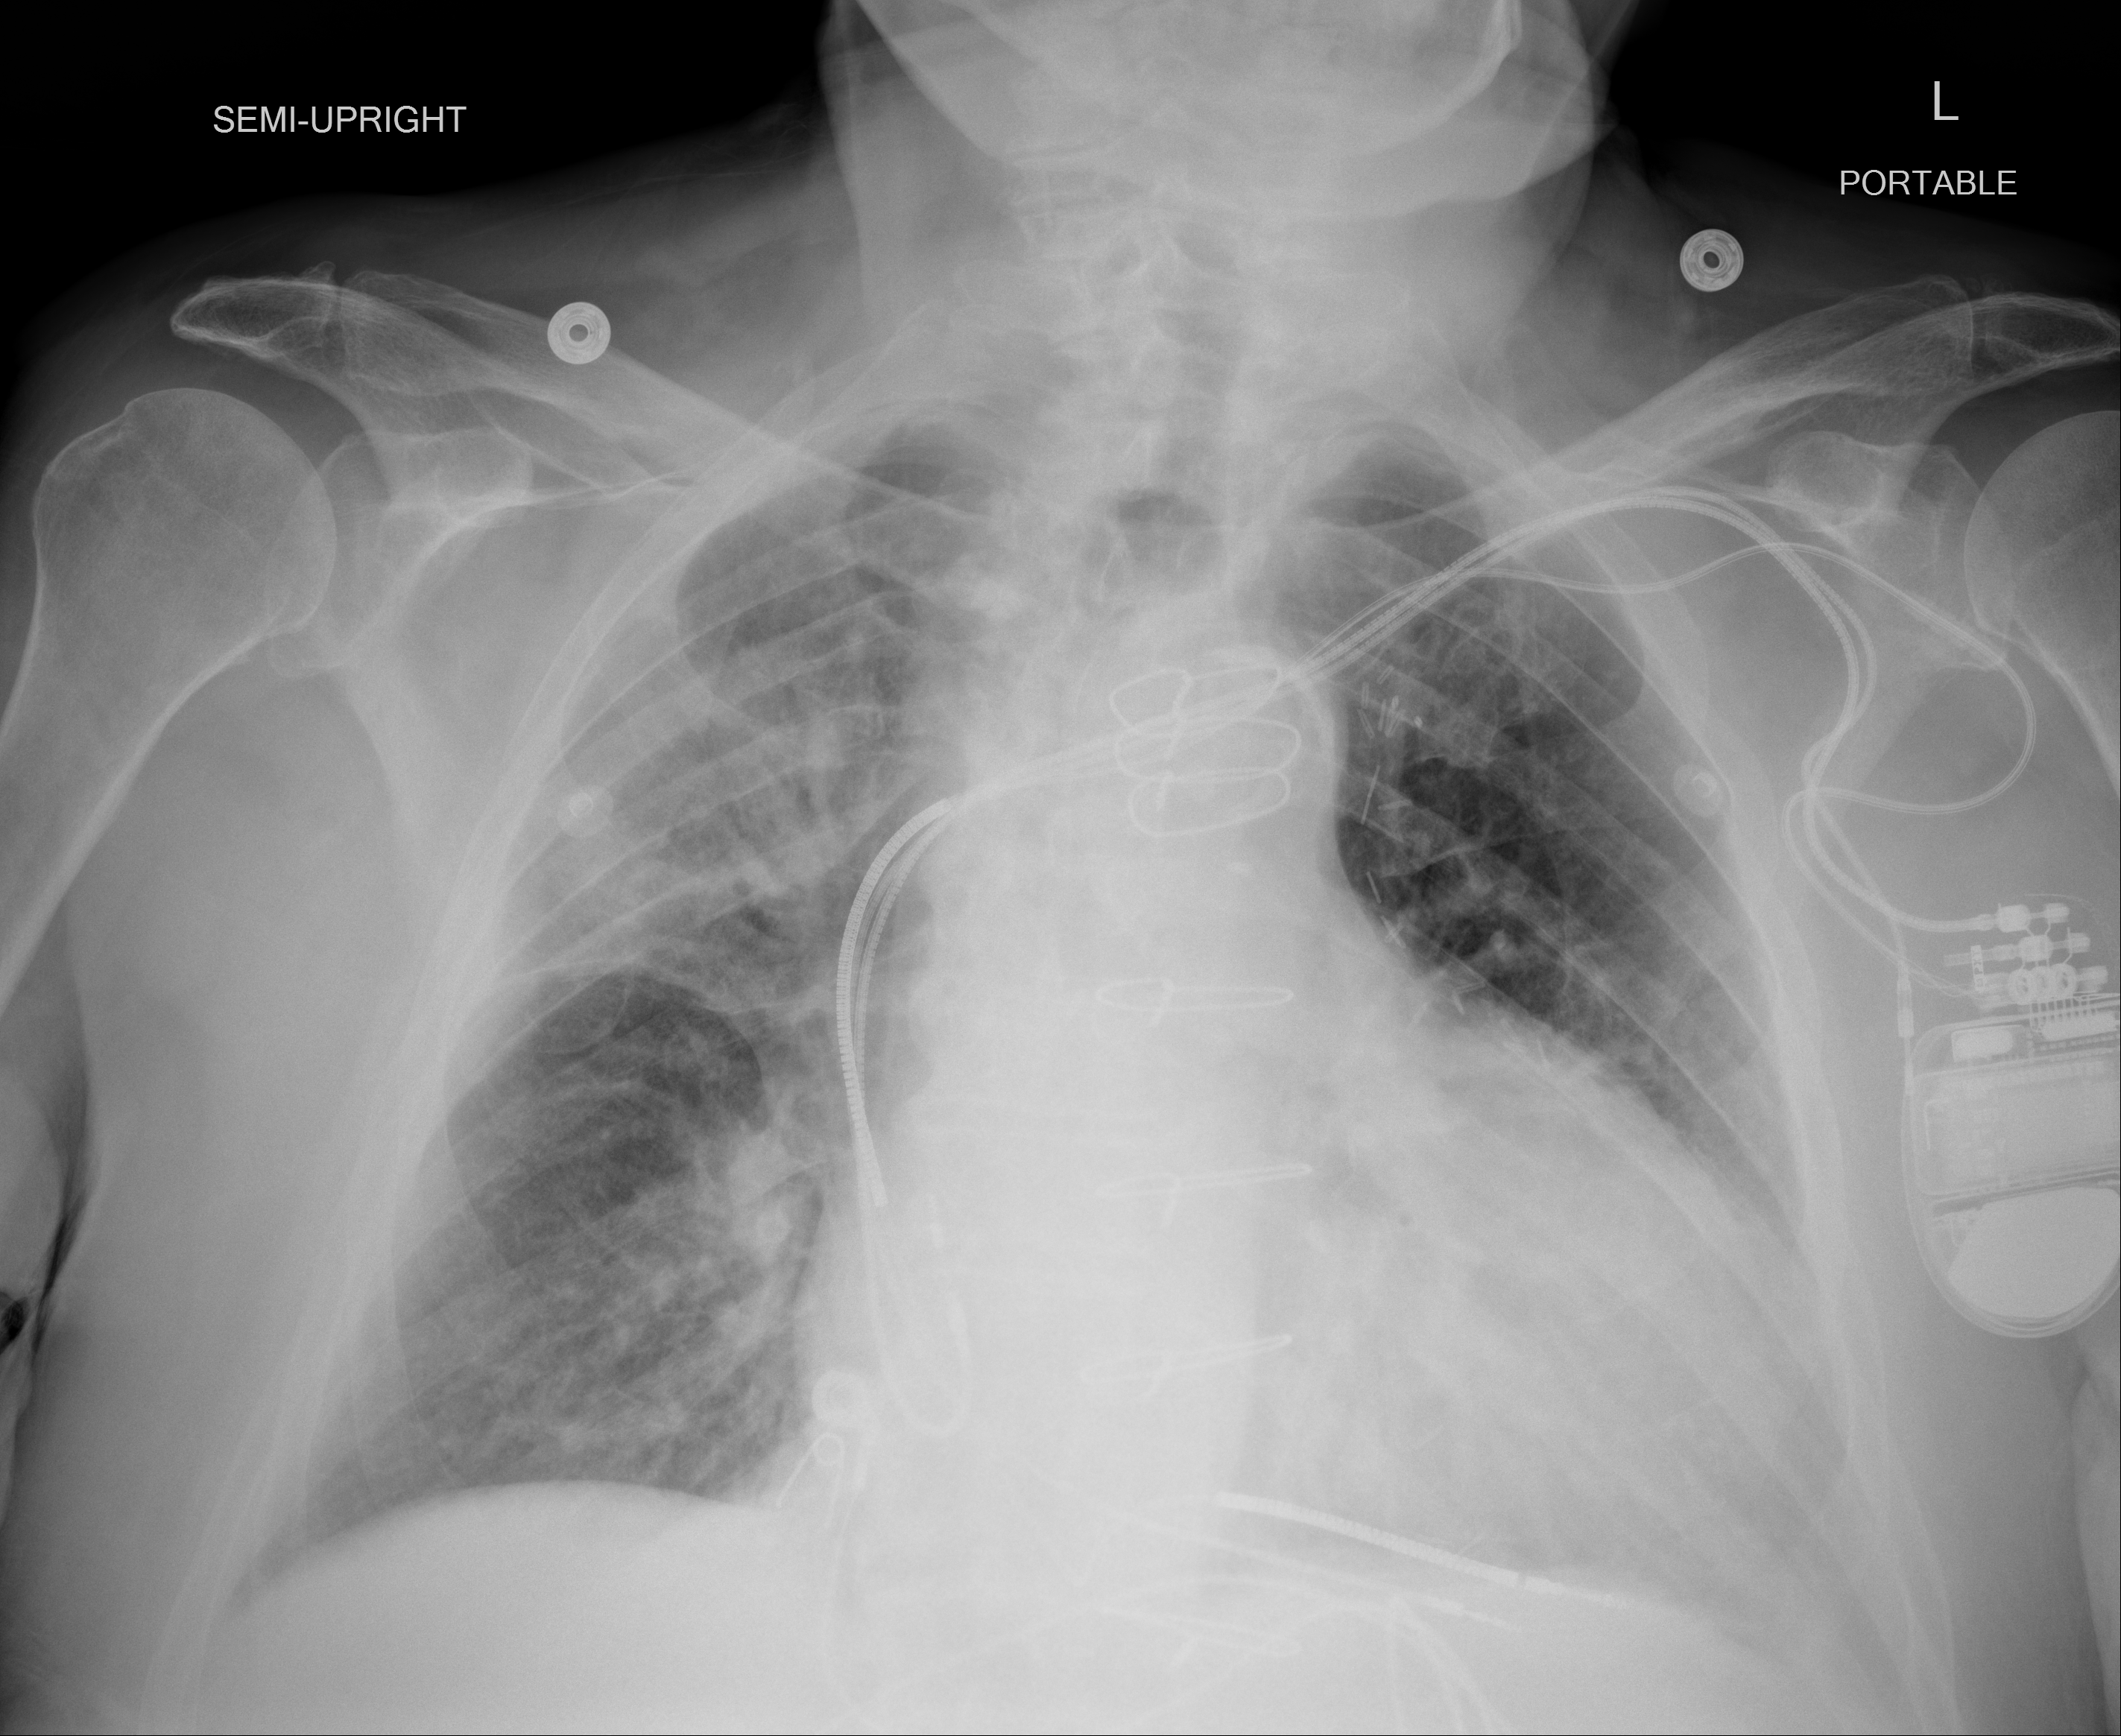
Chest X-ray (portable), AP projection. Male patient, age 87 years; imaged 3 days after the COVID-19 diagnosis.
Key findings recorded by the radiologist: There is increasing airspace opacity in the right upper lobe.